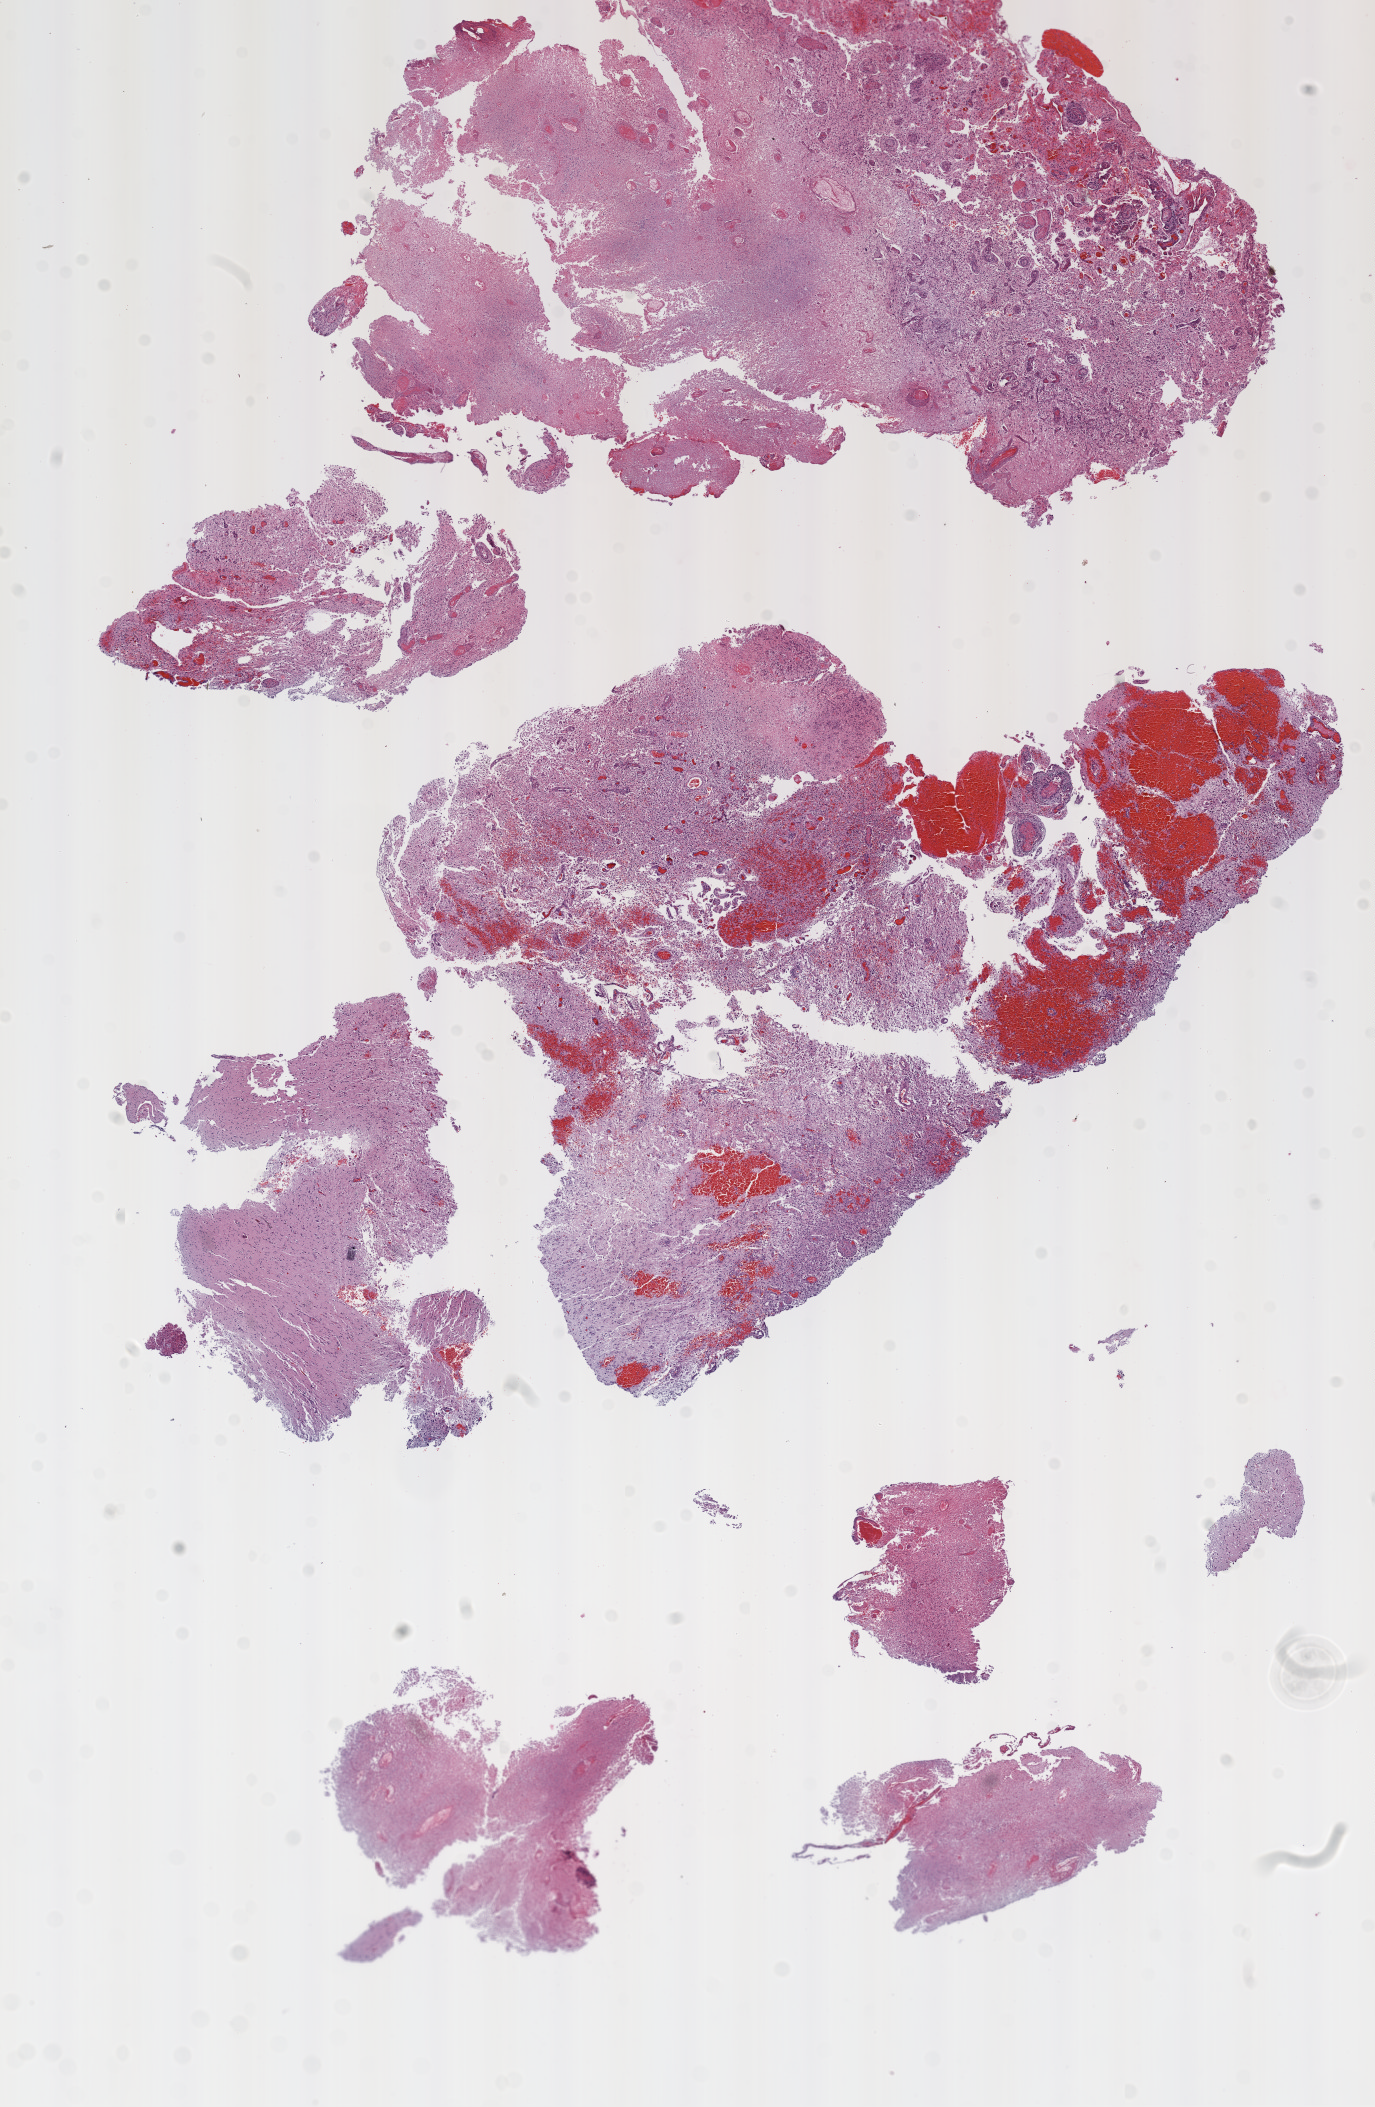
Digitized H&E tissue section (whole slide), a low-resolution overview of the entire scanned area, about 11.0 x 16.9 mm (acquisition: 20x scan). FFPE section. Sample: primary tumour, brain. Patient: male, age at initial diagnosis 40 years.
- histologic diagnosis: Glioblastoma